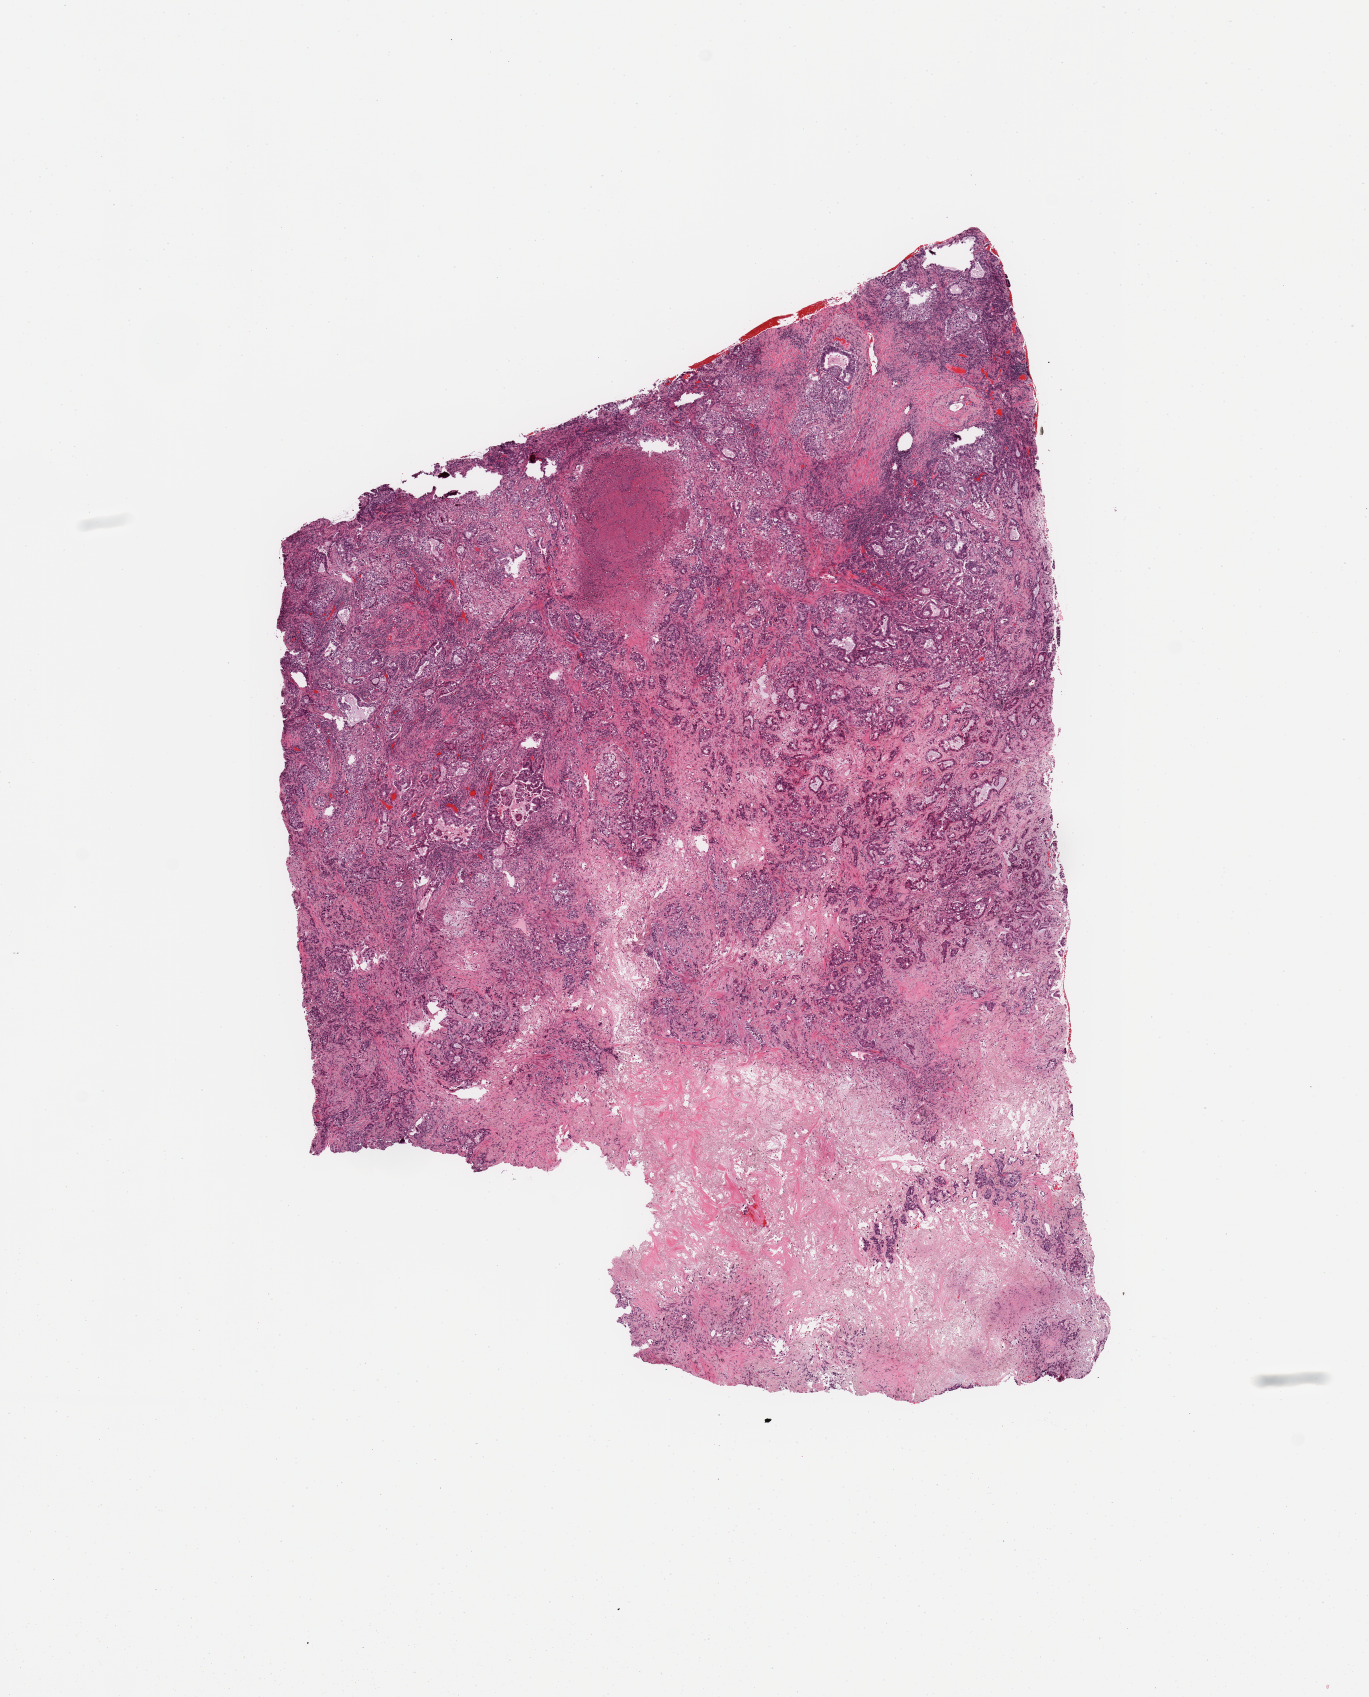
Whole-slide histology image, H&E, shown as a low-resolution overview of the whole scanned area (about 10.8 x 13.4 mm, from a 20x scan), lung, tumour tissue. Patient: female, age 61 years. Histologic grade: G2 (moderately differentiated).
* primary tumour site (as recorded): right upper lobe
* diagnosis: Adenocarcinoma, NOS
* AJCC pathologic stage: IB